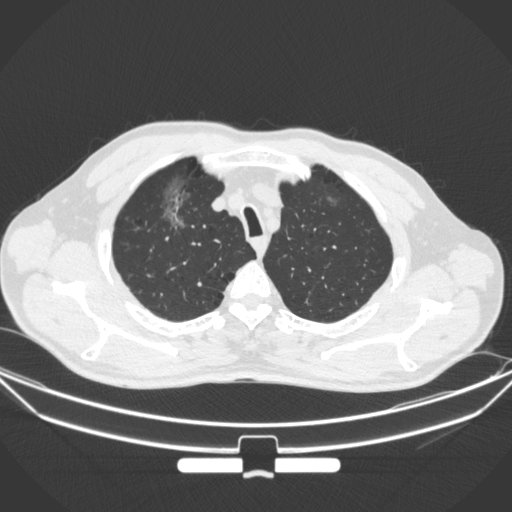
Chest CT, one axial slice. Position 289 of 355 along the scan axis. 120 kVp. Lung window (W 1500 / L -600 HU). 1 mm slice thickness. 512 × 512 image matrix, field of view 399 × 399 mm. Patient: male, 67 years. Case-level facts recorded for this patient, not image findings: clinical TNM (as recorded): T1c N0 M0; histopathological grade: G2.
Structures marked on this image (bounding box drawn by a radiologist):
- lung tumour (recorded histology: adenocarcinoma): box from (x=145, y=165) to (x=194, y=238) px